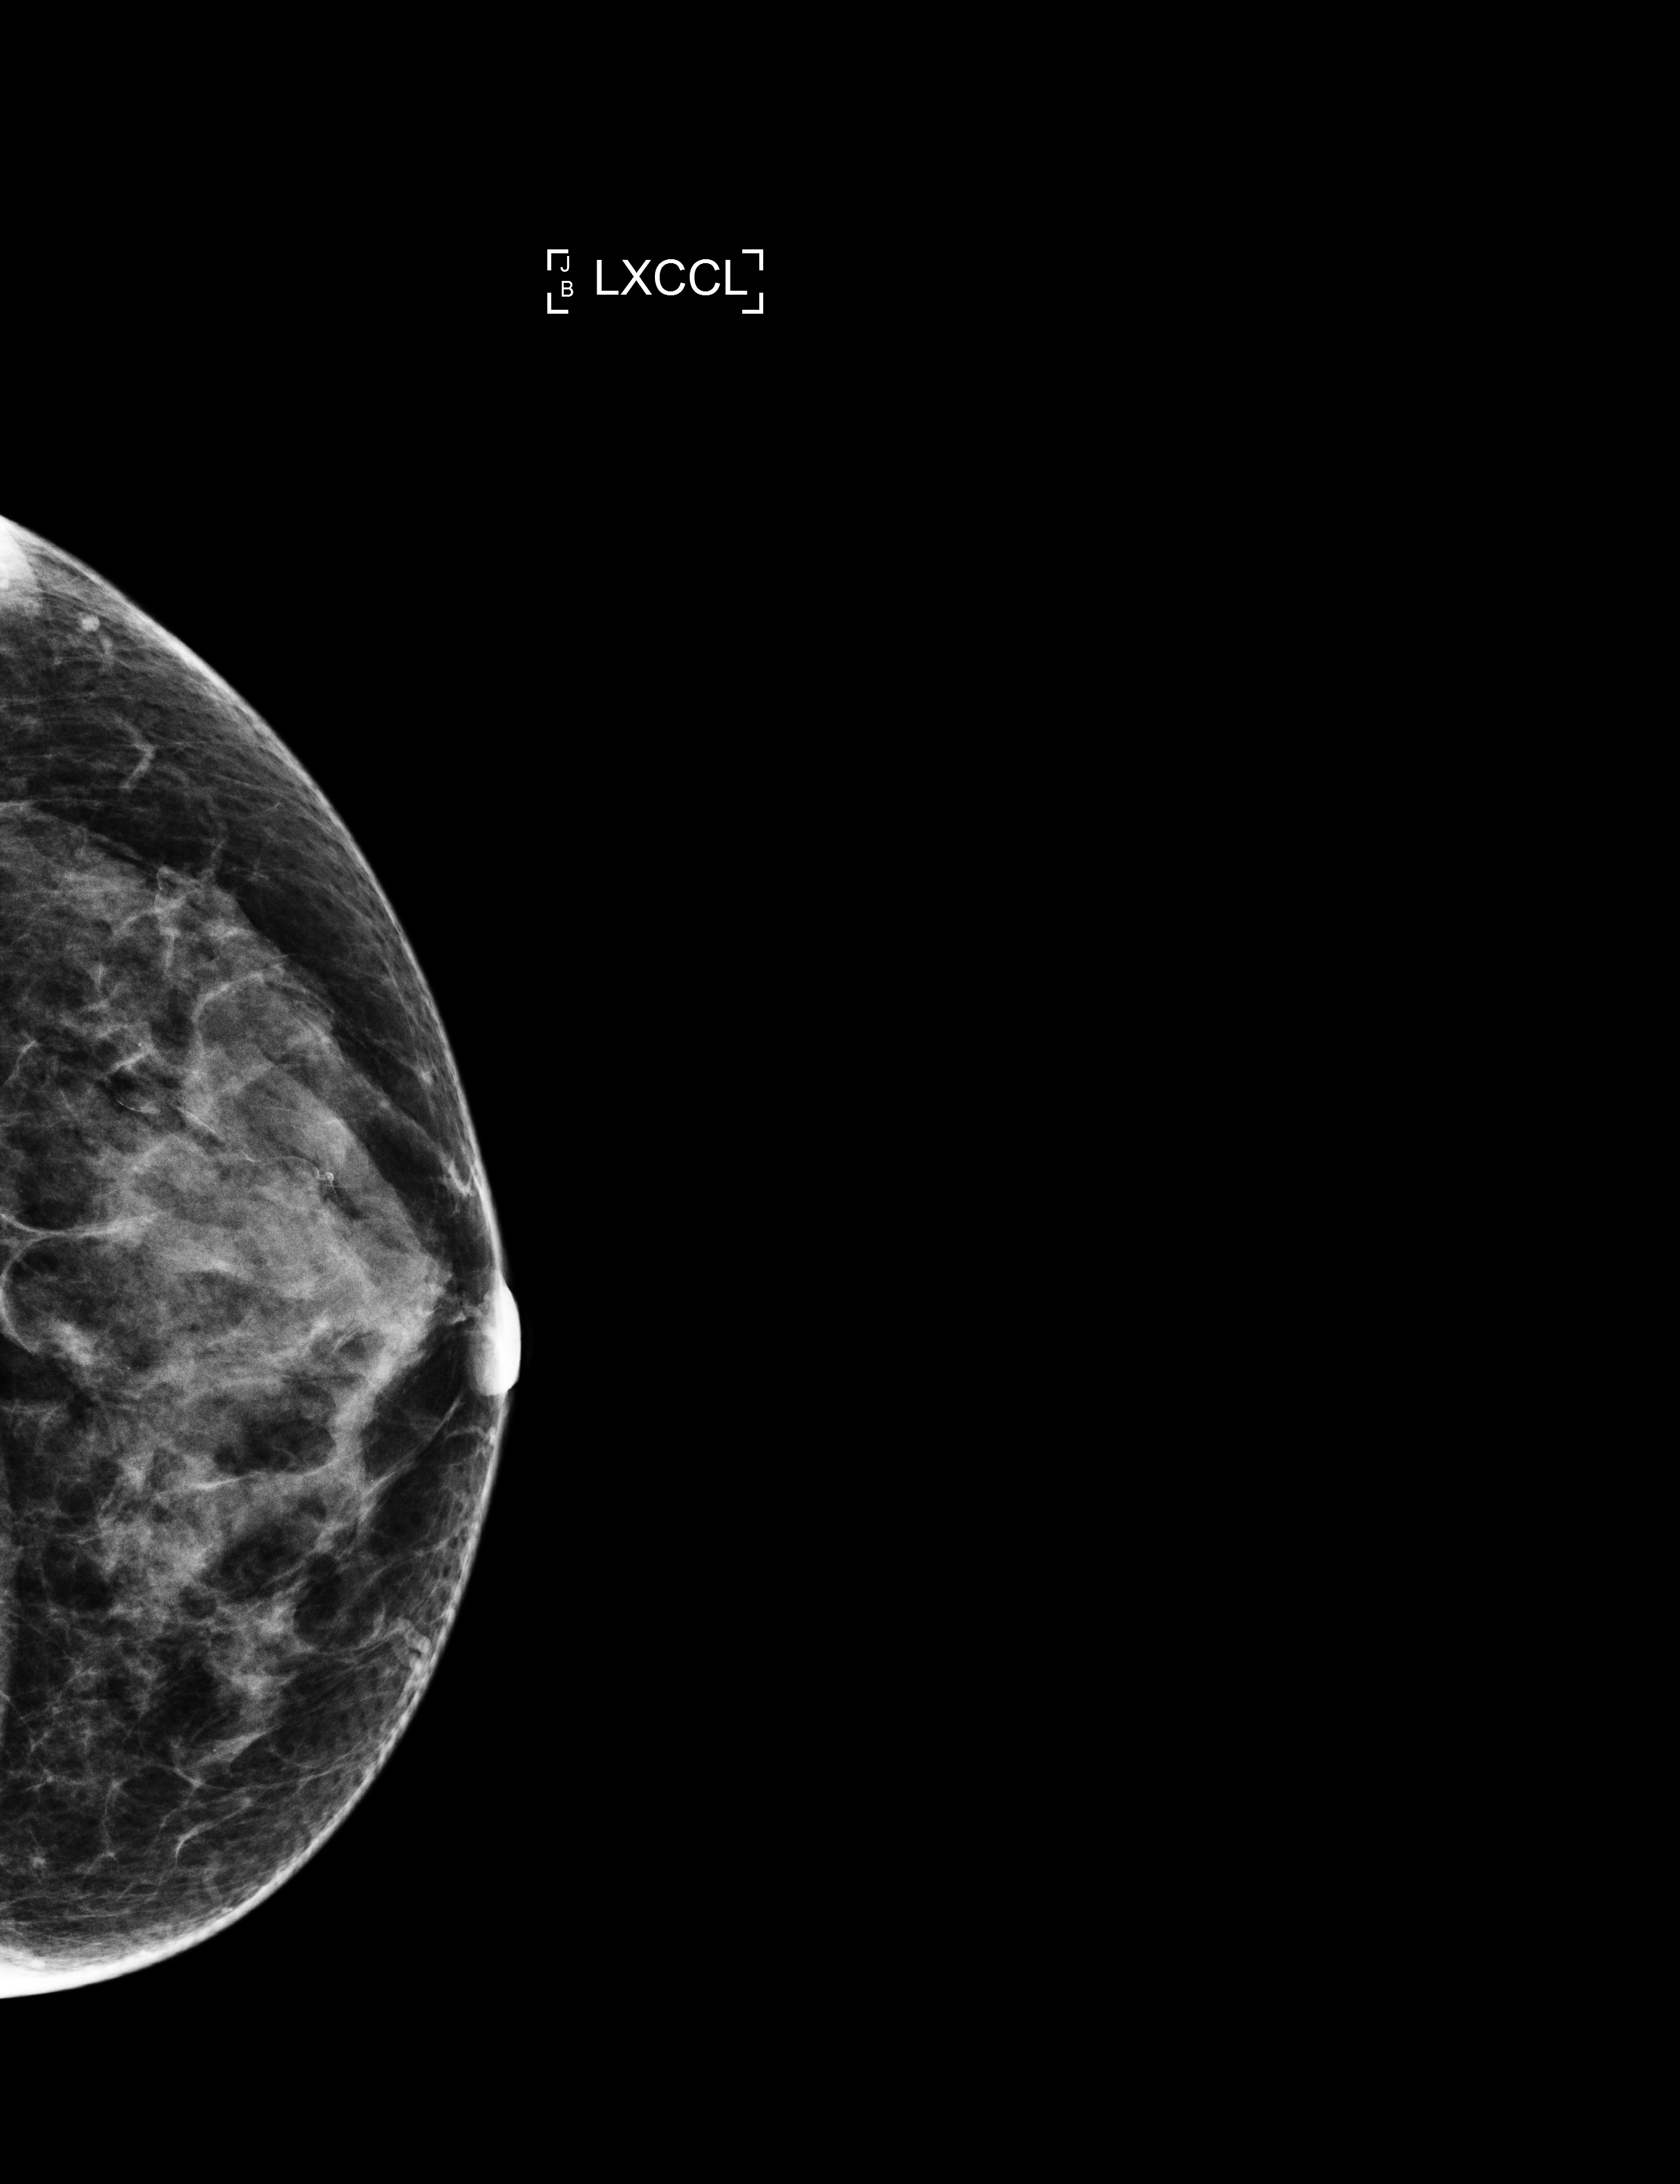
Annual screening mammography examination, compressed breast thickness 39 mm, system: Selenia Dimensions. Female patient, age 58 years.
Image type: full-field digital mammogram. Breast: left. Projection: exaggerated CC view (lateral).